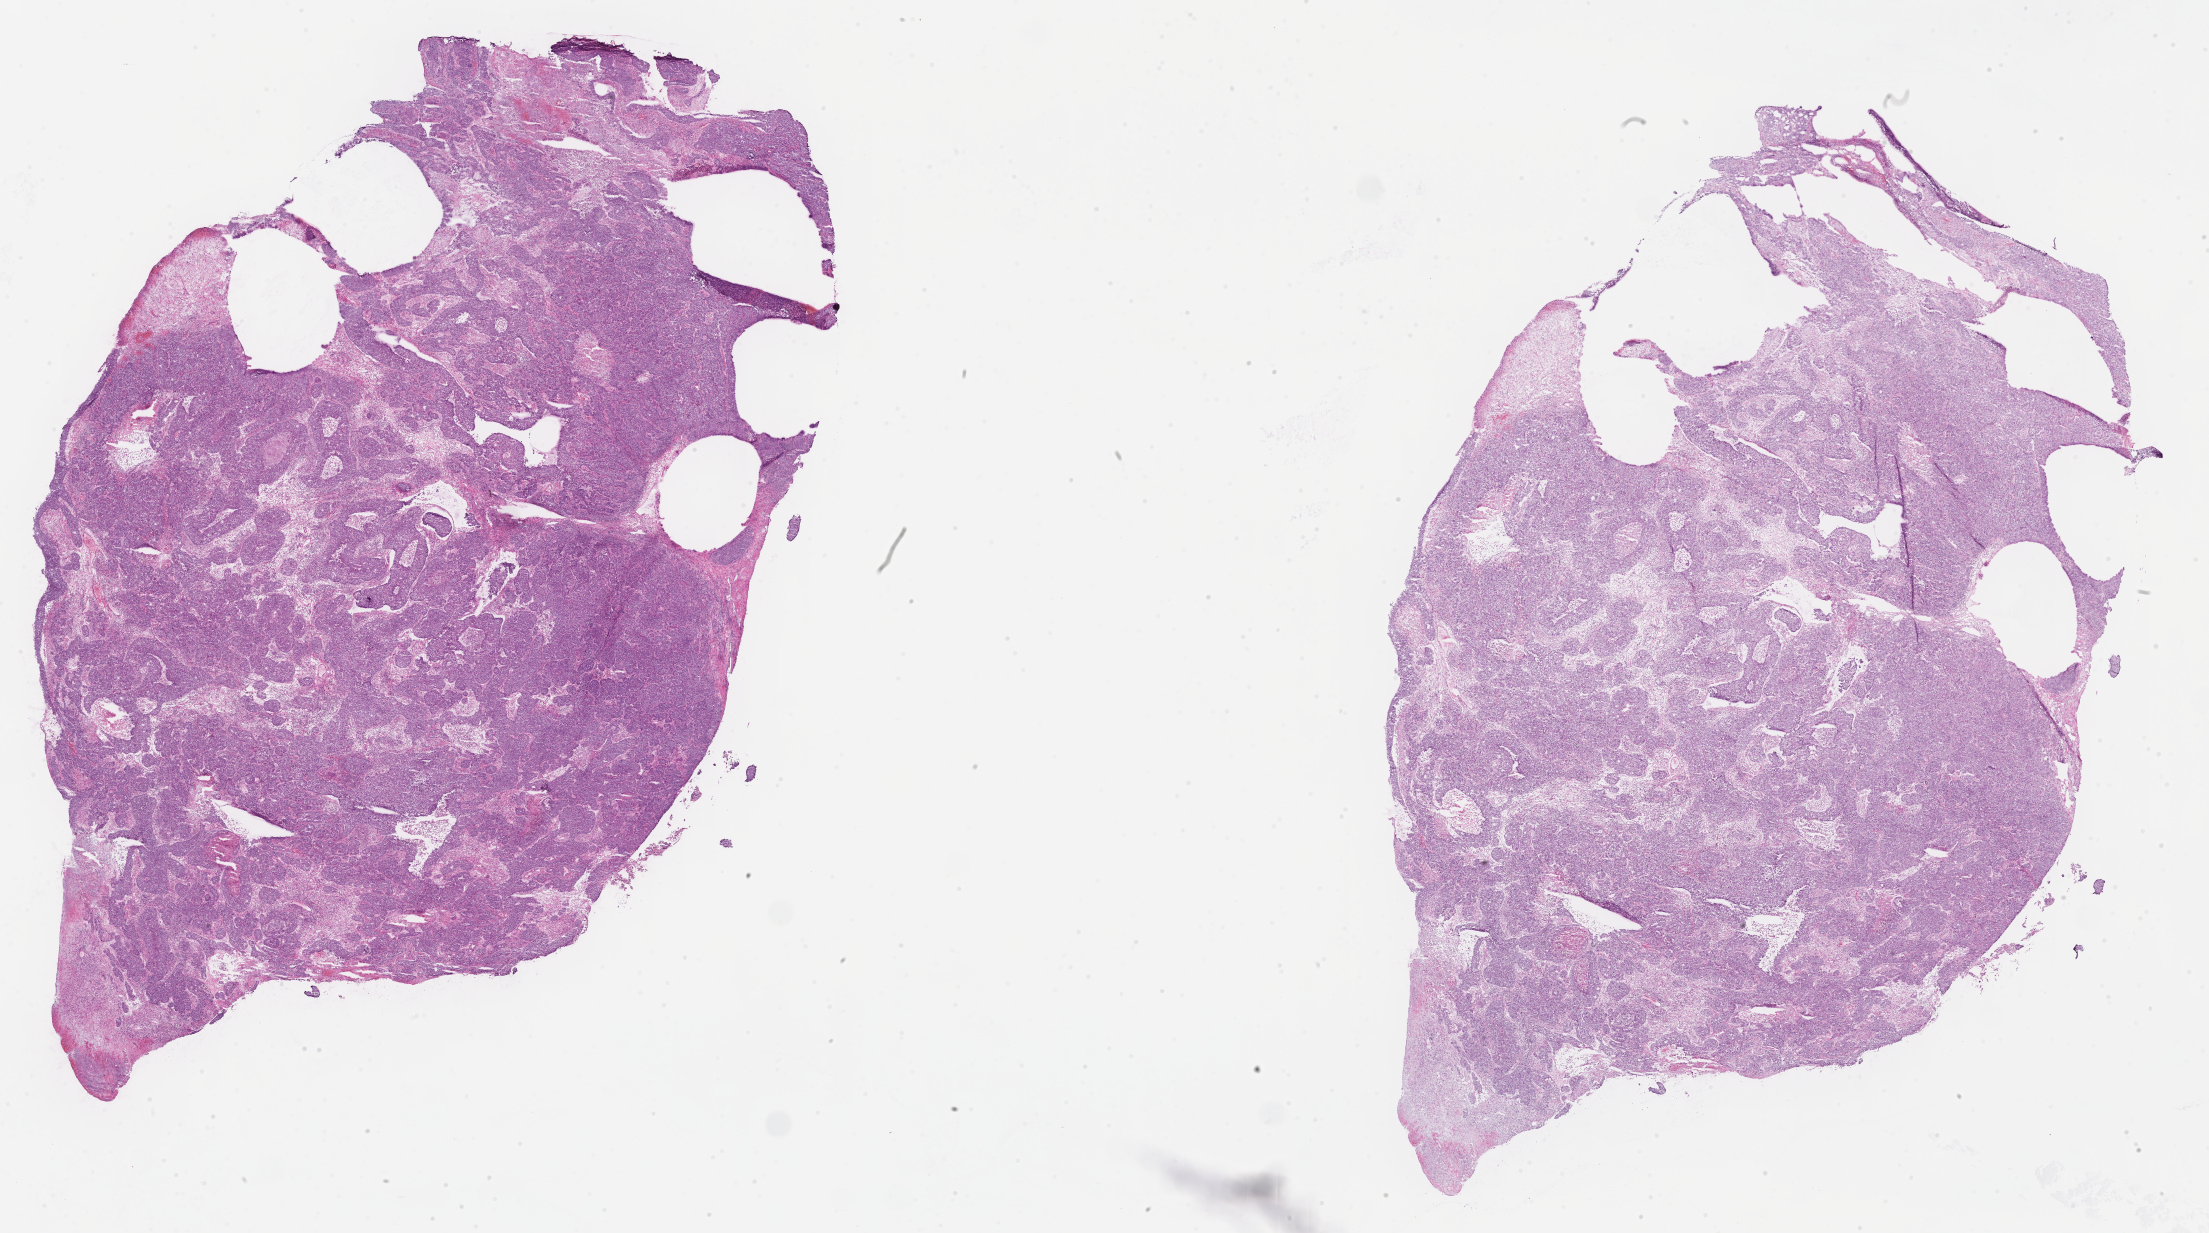
Whole-slide image, haematoxylin and eosin stain — whole scanned area (about 35.7 x 19.9 mm) shown as a low-resolution overview; frozen section; specimen: primary tumor; anatomic site: breast (left). Female, age 86 years at initial diagnosis. Composition of this section per pathologist review: tumor cells 80%, tumor nuclei 80%, stromal cells 18%, necrosis 2%, normal cells 0%. Inflammatory infiltration, as recorded: lymphocyte infiltration 5%, monocyte infiltration 1%, neutrophil infiltration 8%.
Diagnosis: Infiltrating duct carcinoma, NOS.